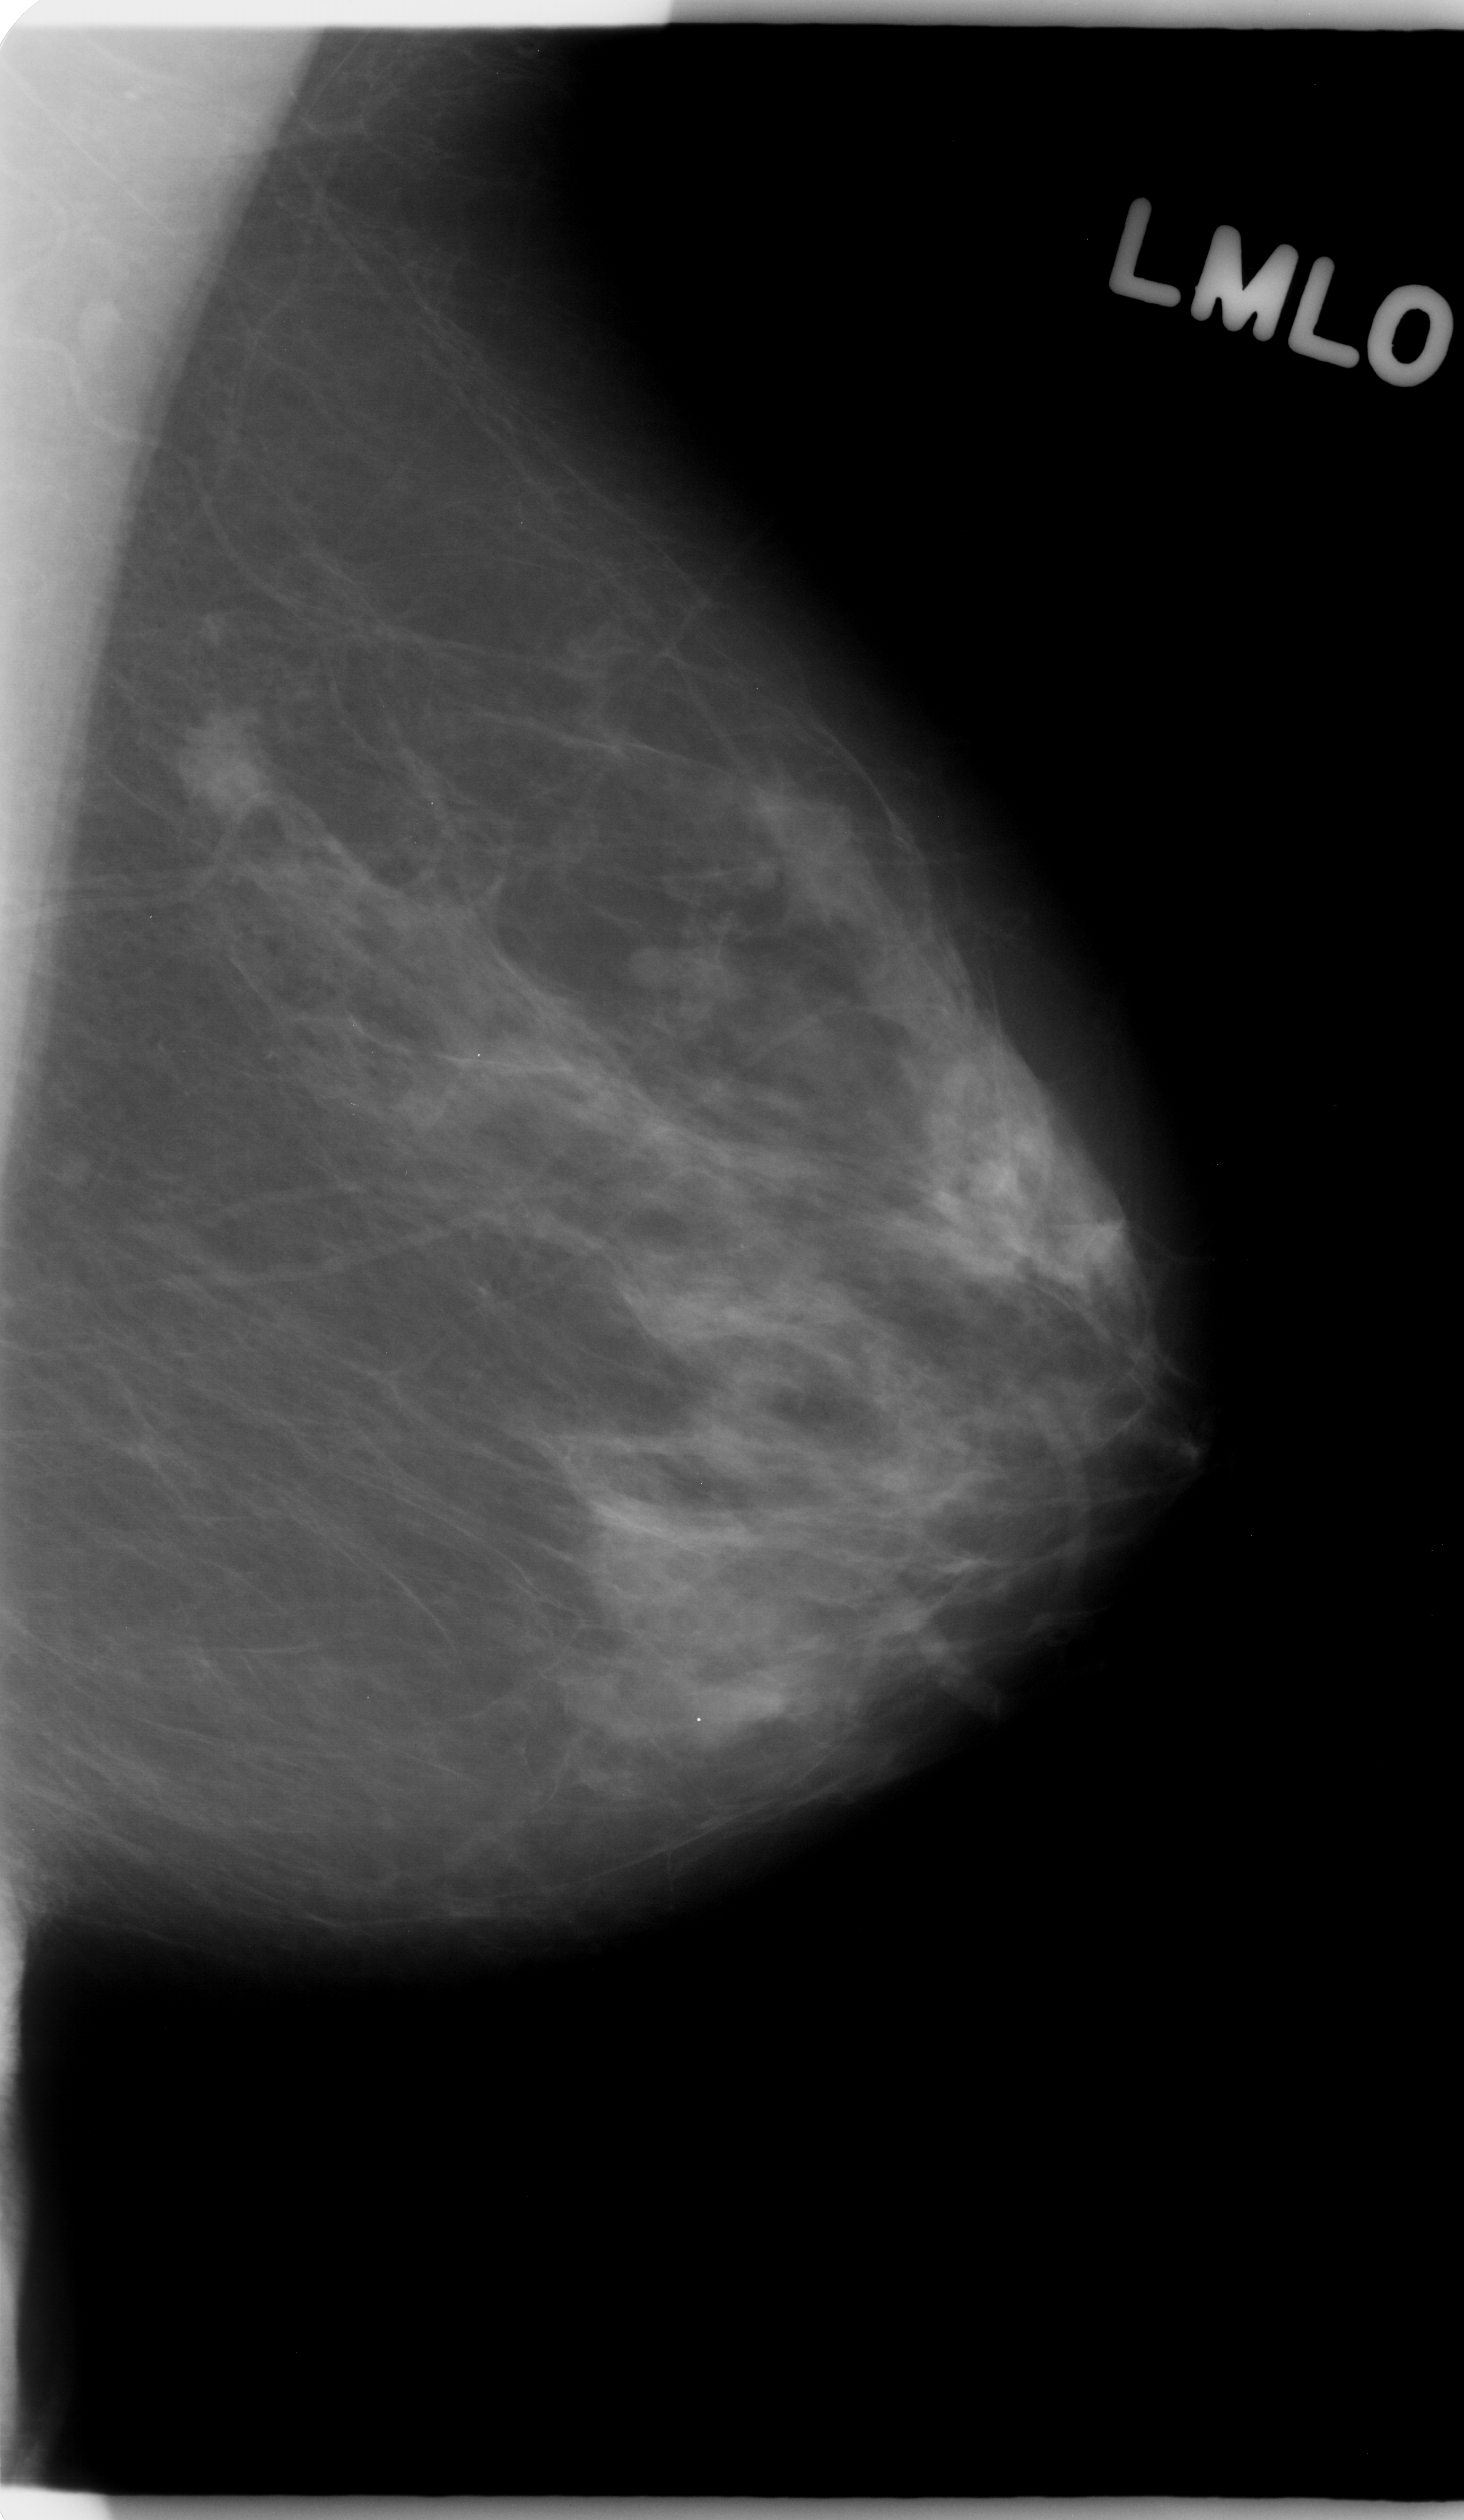
Scanned film-screen mammogram, left breast, MLO view, breast composition: scattered fibroglandular densities (BI-RADS density category 2 of 4).
Radiologist-marked abnormalities on this image: mass, shape irregular, margins microlobulated; BI-RADS assessment category 4; pathology (as recorded): malignant.